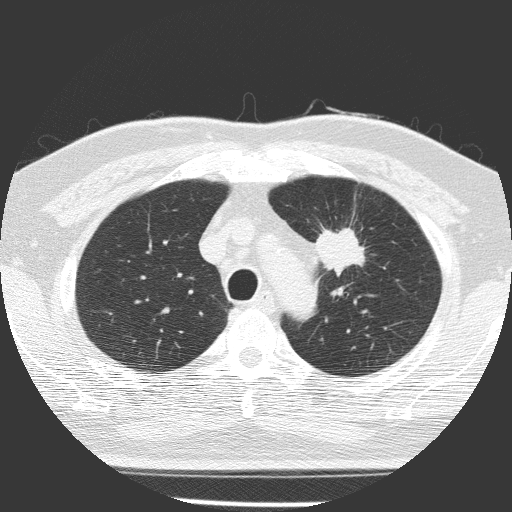
Low-dose screening chest CT, axial slice; first (baseline) screen; lung window (W 1500 / L -600 HU); lung (sharp) reconstruction kernel (FC51). Male participant, aged 70 years at enrolment. Current smoker at enrolment.
Expert reader's lesion annotation, bounding box <297,220,372,294> (left, top, right, bottom; pixels). The screening reader recorded 3 non-calcified nodules or masses ≥4 mm on this exam; which of them this box marks is not recorded. Lung cancer was diagnosed 58 days after this screen: squamous cell carcinoma, NOS, left upper lobe, poorly differentiated (G3), stage IB (AJCC 6th edition), 47 mm at pathology.